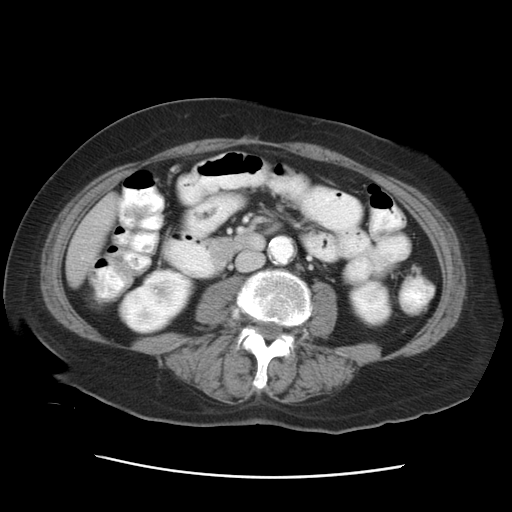
Contrast-enhanced abdominal CT, one axial slice. Position 7 of 29 along the scan axis. 120 kVp. Intravenous contrast given. Soft-tissue window (W 400 / L 40 HU). 512 × 512 image matrix. Female patient, age 64 years. Case-level facts recorded for this patient, not image findings: diagnosis: colorectal cancer liver metastases, imaged before liver resection; multiple liver metastases: no; largest metastasis: 2.5 cm; disease in both lobes: no.
Annotated regions visible in this slice (outlined manually by an expert reader):
- liver: bounding box [x1, y1, x2, y2] px = [67, 196, 117, 286]
- planned liver remnant (the part of the liver to remain after resection): [67, 196, 117, 286]